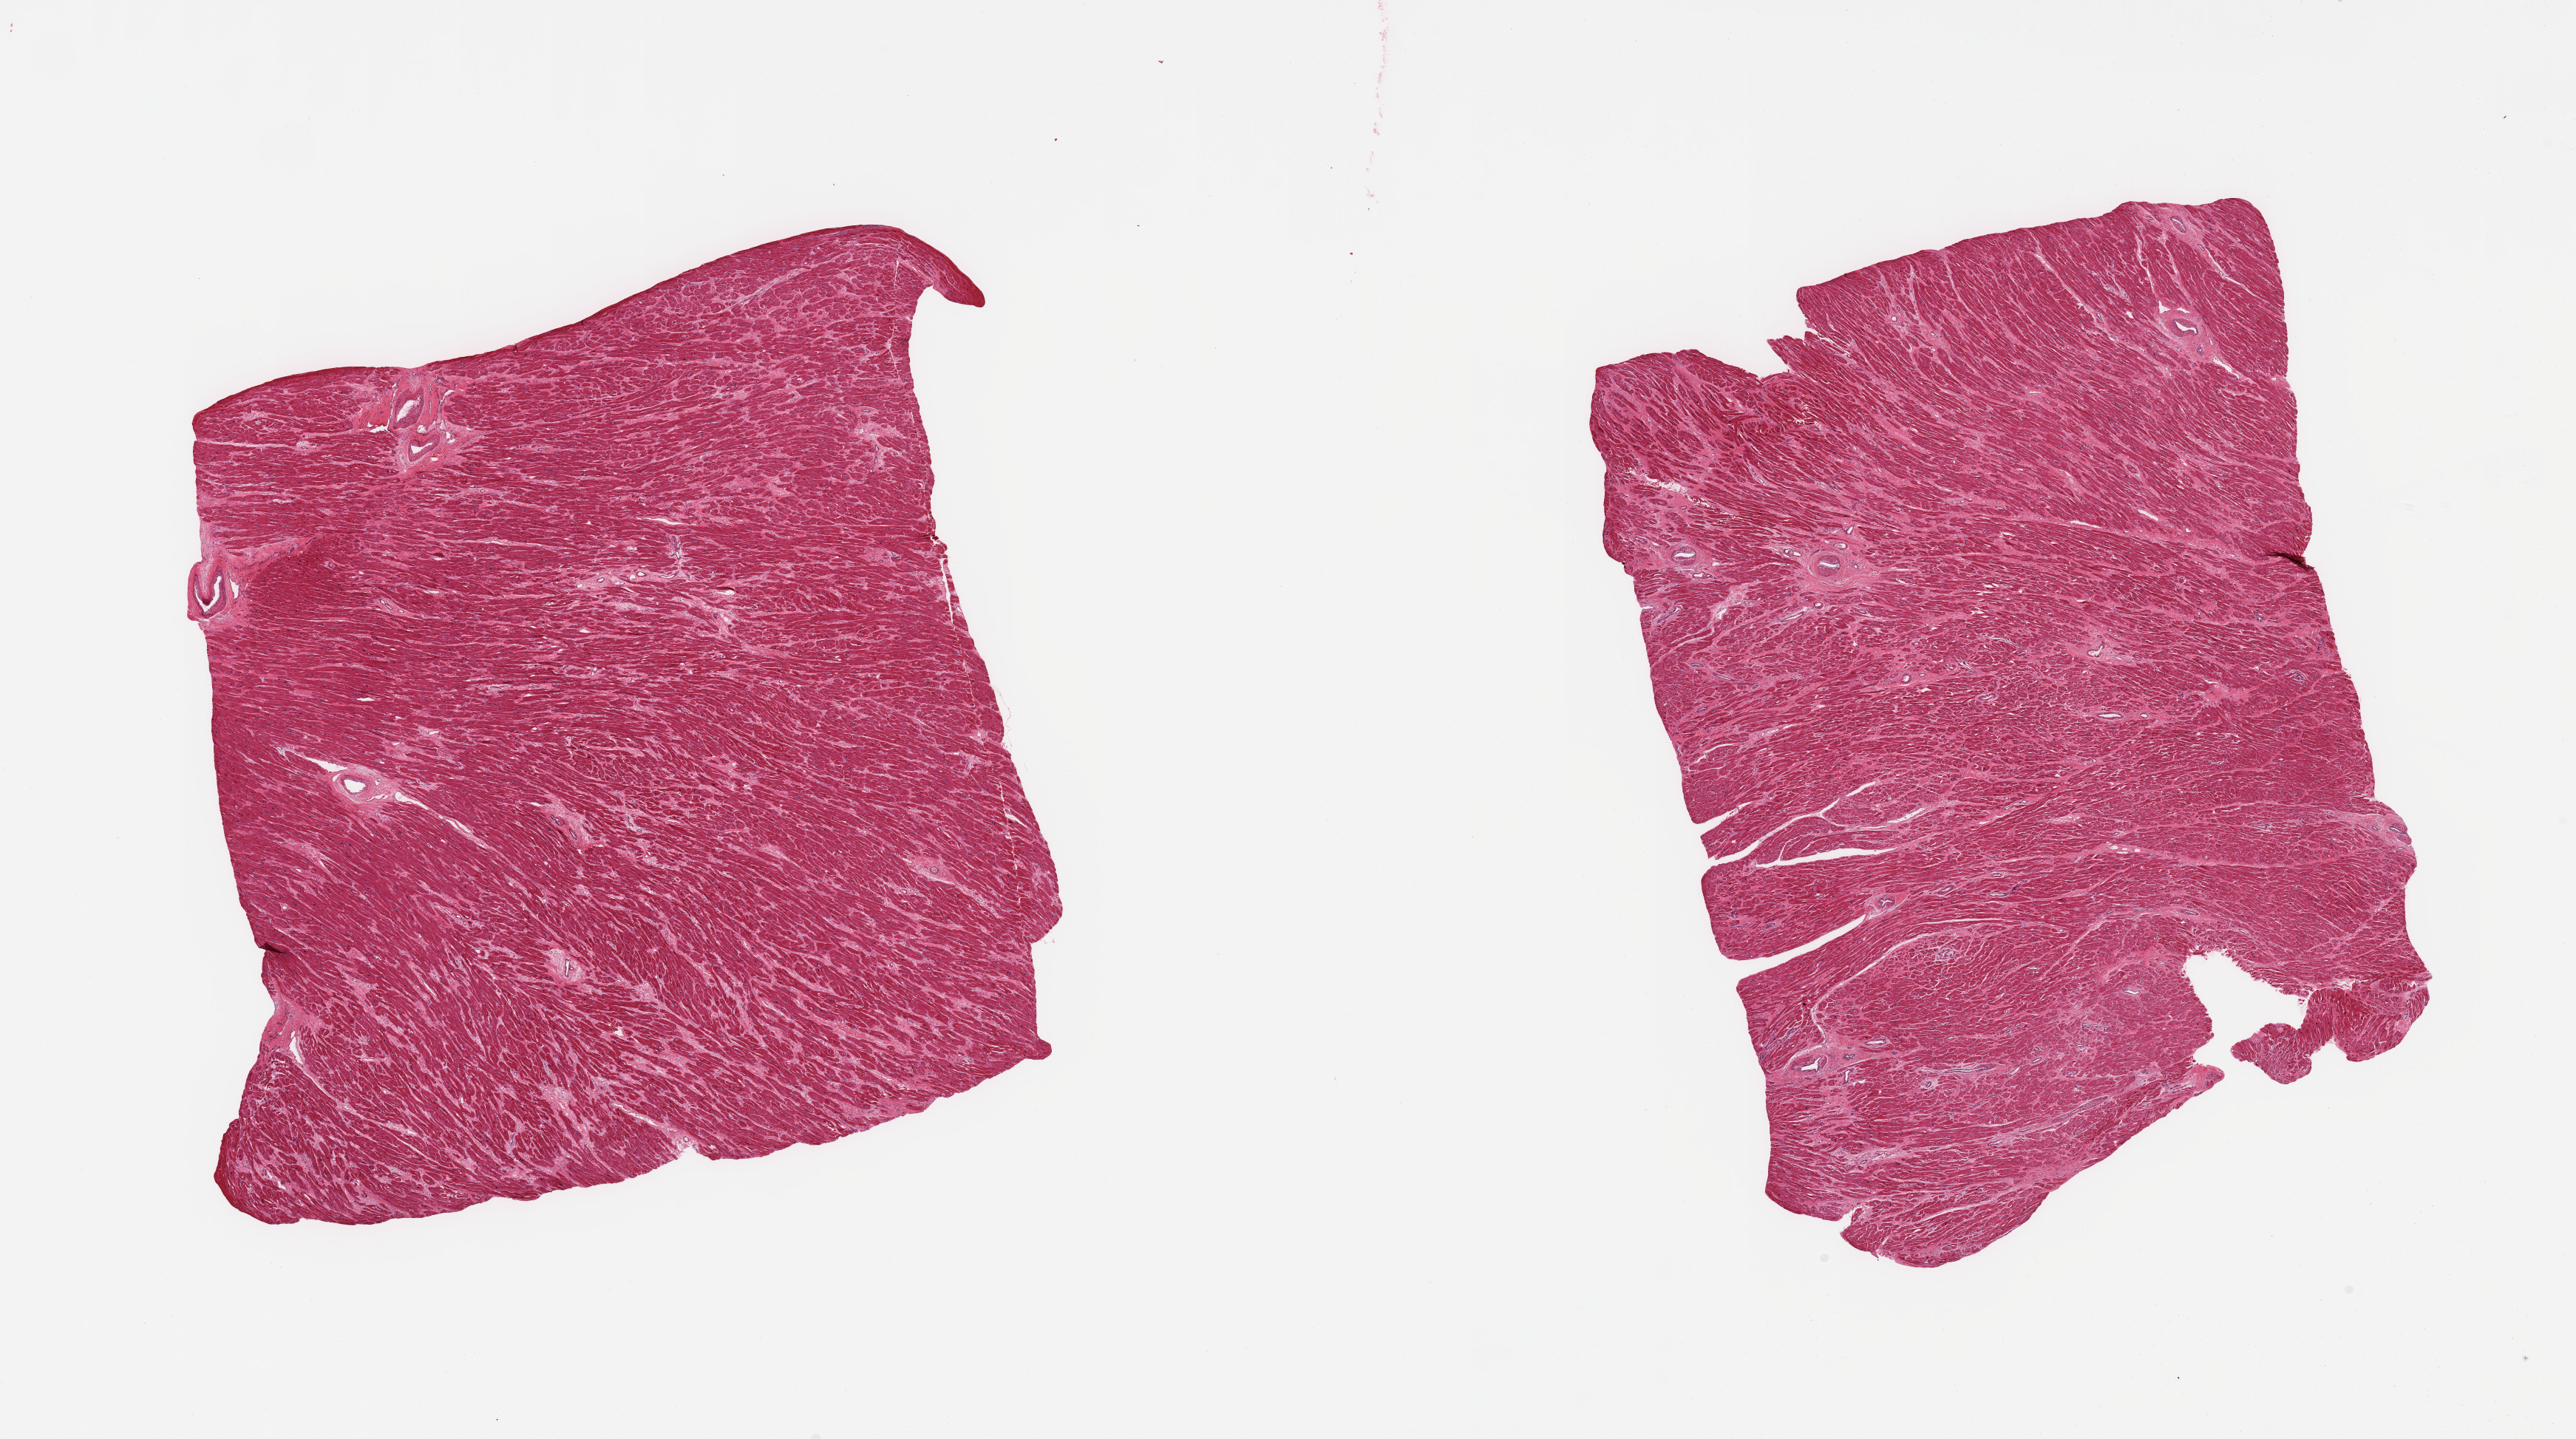
Digitized hematoxylin and eosin (H&E)-stained section — low-resolution overview of the scanned area, about 27.6 x 15.4 mm; PAXgene-fixed paraffin-embedded (PFPE) section; target tissue: heart; tissue donor sample. Donor sex: male.
Pathologist's review note for this sample: 2 pieces; 5-10% interstitial fibrosis.